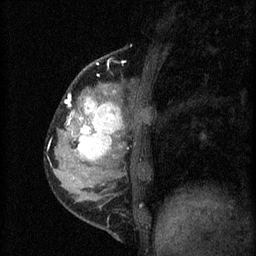
Breast MRI (dynamic contrast-enhanced), one sagittal slice. Position 16 of 60 along the scan axis. 3 images stored at this slice position (order not interpretable as contrast timing). 1.5 T. TE 4.2 ms, TR 8.2 ms. 2 mm slice thickness. 256 × 256 image matrix, field of view 180 × 180 mm. Female patient, age 37 years.
Structures marked on this image (semi-automatically segmented with operator editing):
- analysis volume of interest (the breast-tissue region the enhancement analysis was run in; not a lesion): bounding box [x1, y1, x2, y2] px = [53, 78, 140, 181]
- tumour enhancement mask (voxels above the 70 % enhancement threshold inside the analysis volume of interest): [67, 94, 123, 161]